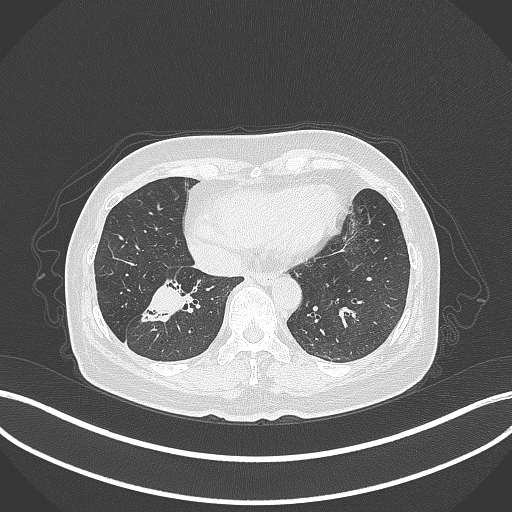
Chest CT, one axial slice. Lung window (W 1500 / L -600 HU). 1 mm slice thickness. 512 × 512 image matrix. Female patient, age 67 years. From the clinical record (not read from this slice): clinical TNM (as recorded): T1c N1 M0.
Outlined on this slice (rectangle marked by the reading radiologist):
- lung tumour (recorded histology: adenocarcinoma): box from (x=138, y=277) to (x=189, y=325) px